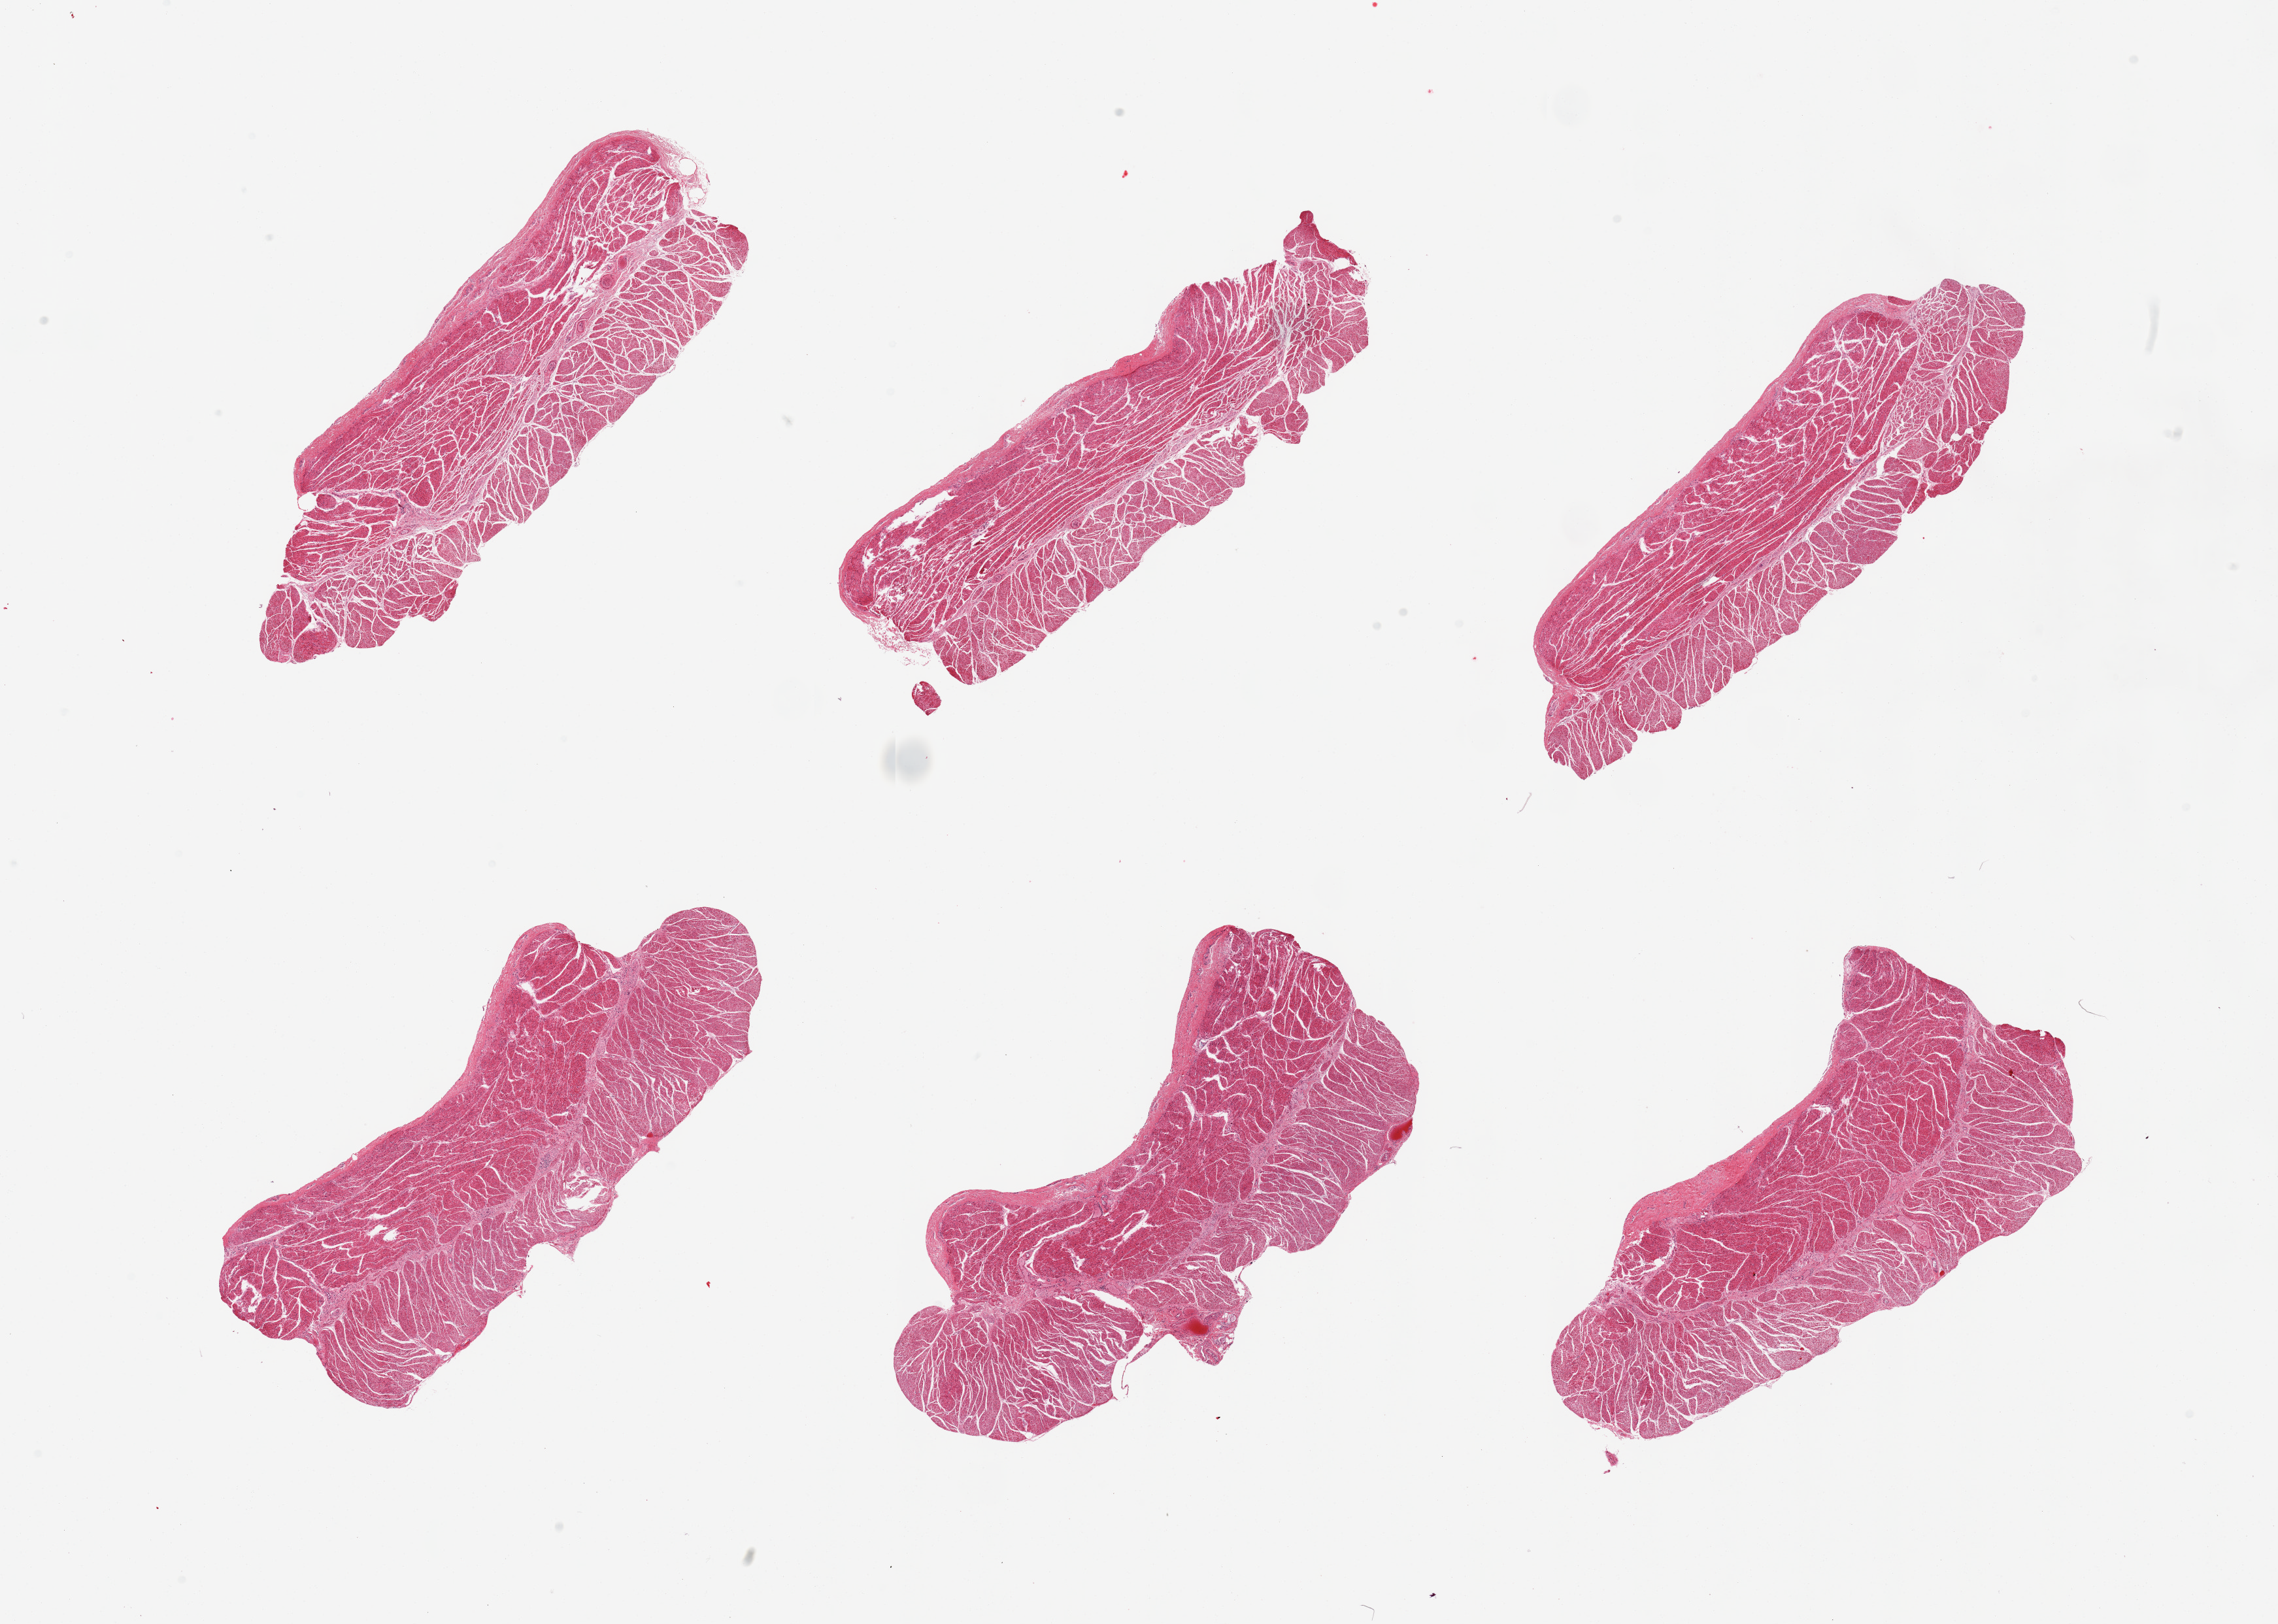
Digitized haematoxylin and eosin-stained section — whole scanned area (about 27.6 x 19.7 mm) shown as a low-resolution overview; PAXgene-fixed paraffin-embedded (PFPE) section; target tissue: esophageal muscle; tissue donor sample. Male donor.
• review note (as recorded): 6 pieces; well trimmed